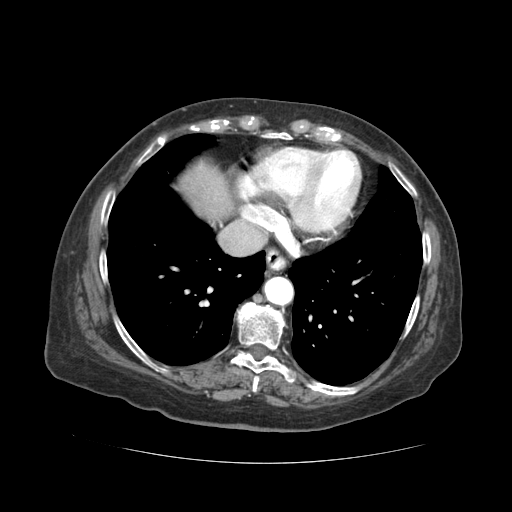
Contrast-enhanced abdominal CT (liver protocol), one axial slice; position 48 of 59 along the scan axis; 120 kVp; soft-tissue window (W 400 / L 40 HU); 2.5 mm slice thickness; 512 × 512 image matrix. From the clinical record (not read from this slice): diagnosis: hepatocellular carcinoma (patient treated with transarterial chemoembolisation; whether this scan precedes or follows treatment is not stated here); TNM stage (as recorded): Stage-I; Child-Pugh class: A; tumour nodularity: uninodular.
Annotated regions visible in this slice (semi-automatically segmented with operator editing):
- liver parenchyma outside the tumour (the mass and vessels are separate outlines, so this box may not span the whole liver): bounding box (x1, y1, x2, y2) in pixels: (180, 164, 232, 218)